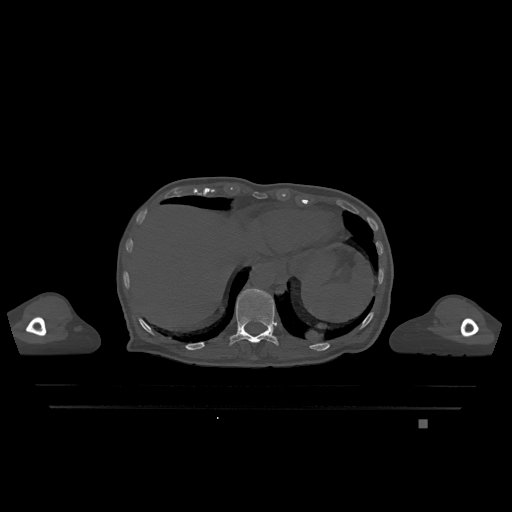
CT including the spine, one axial slice; position 590 of 1317 along the scan axis; bone window (W 1800 / L 400 HU); 0.5 mm slice thickness; 512 × 512 image matrix, field of view 500 × 500 mm. Female patient, age 74 years. From the clinical record (not read from this slice): primary cancer: lung.
Structures marked on this image (semi-automatic segmentation, software-assisted and operator-edited):
- T11 vertebra: bounding box <229,289,279,346> (left, top, right, bottom; pixels)